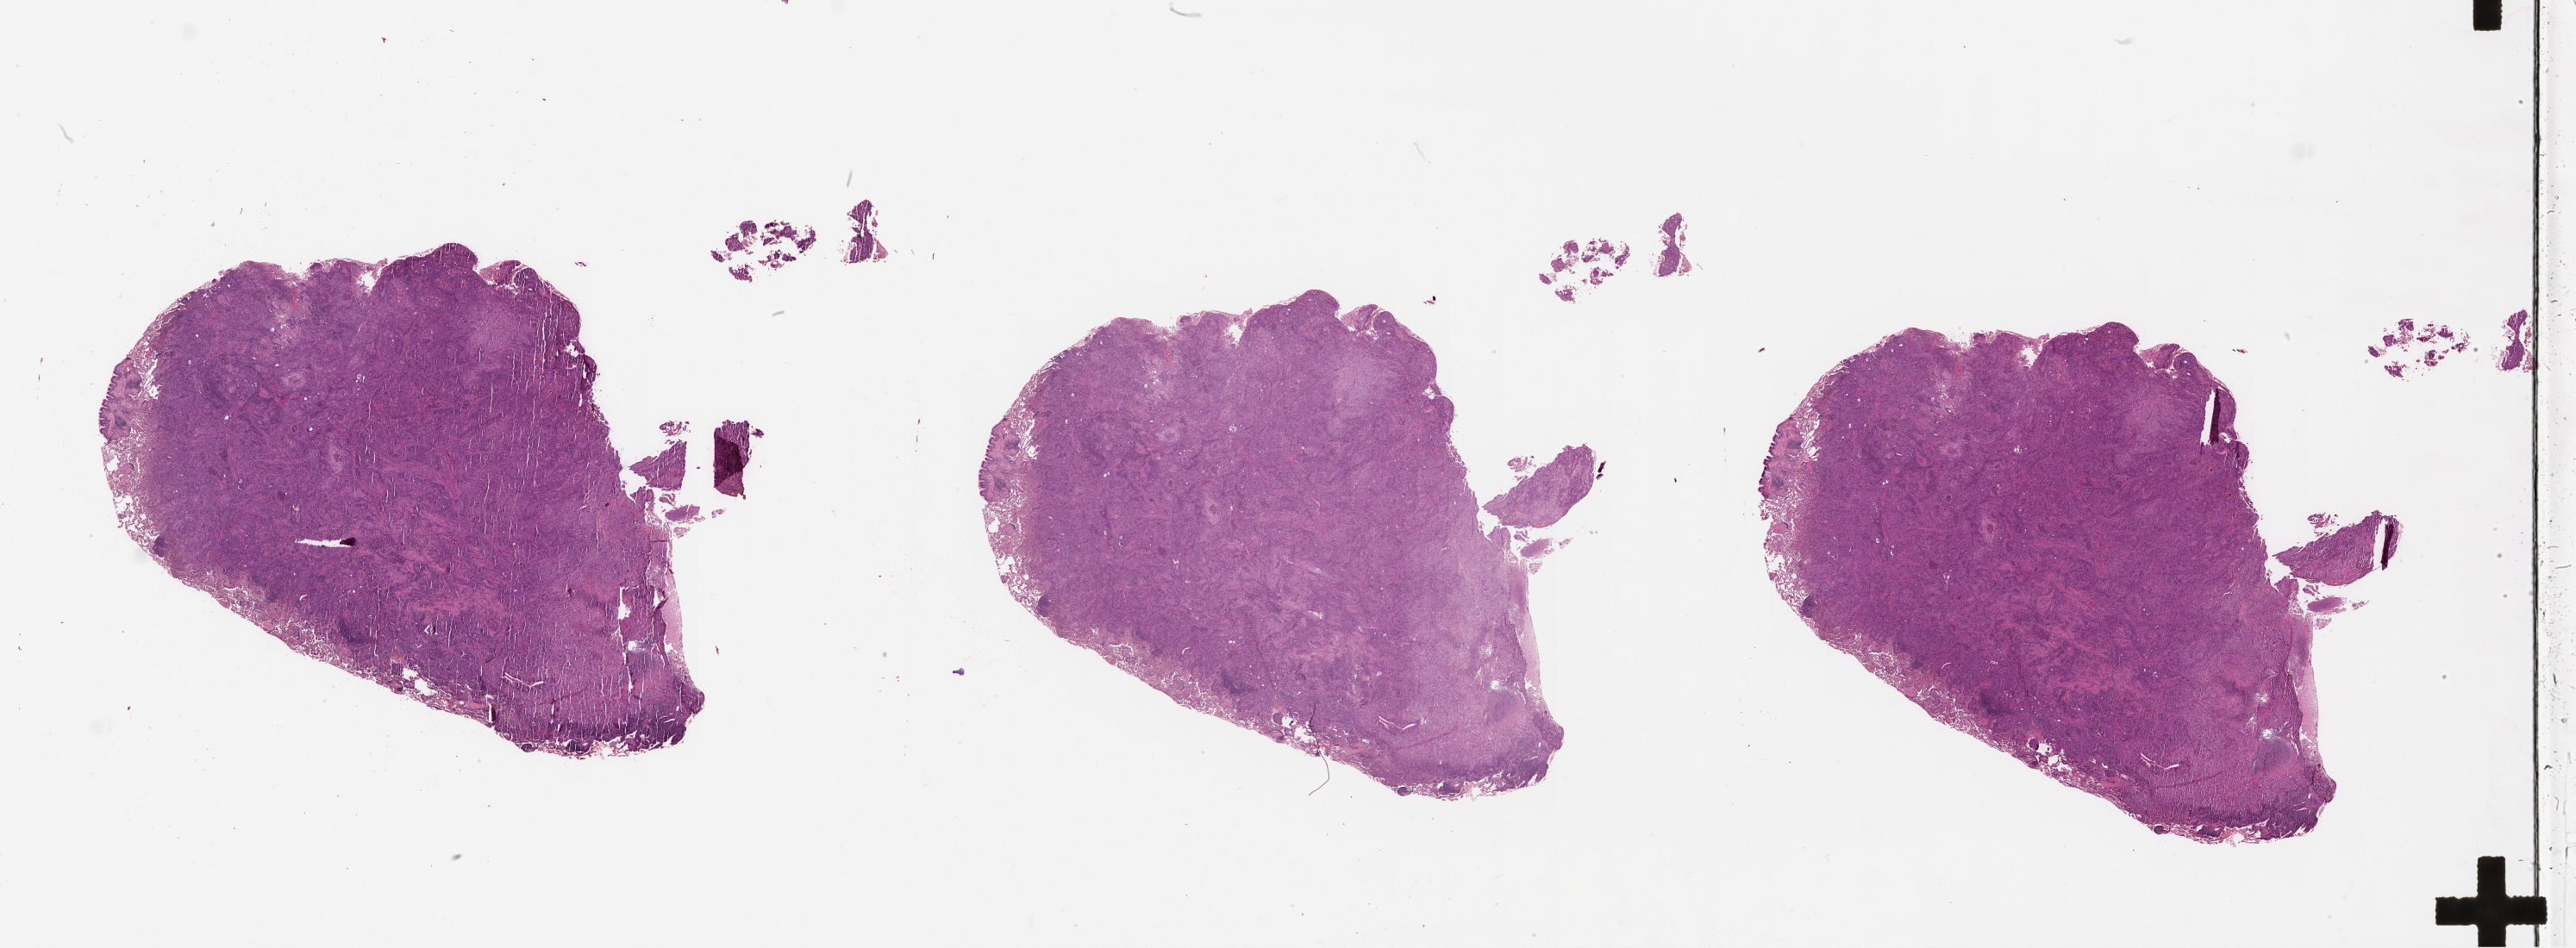
H&E-stained whole-slide image, whole scanned area (about 48.1 x 17.7 mm) shown as a low-resolution overview, lung, tumour tissue. 77-year-old male patient.
Patient diagnosis (cohort enrolment): squamous cell carcinoma (lung).